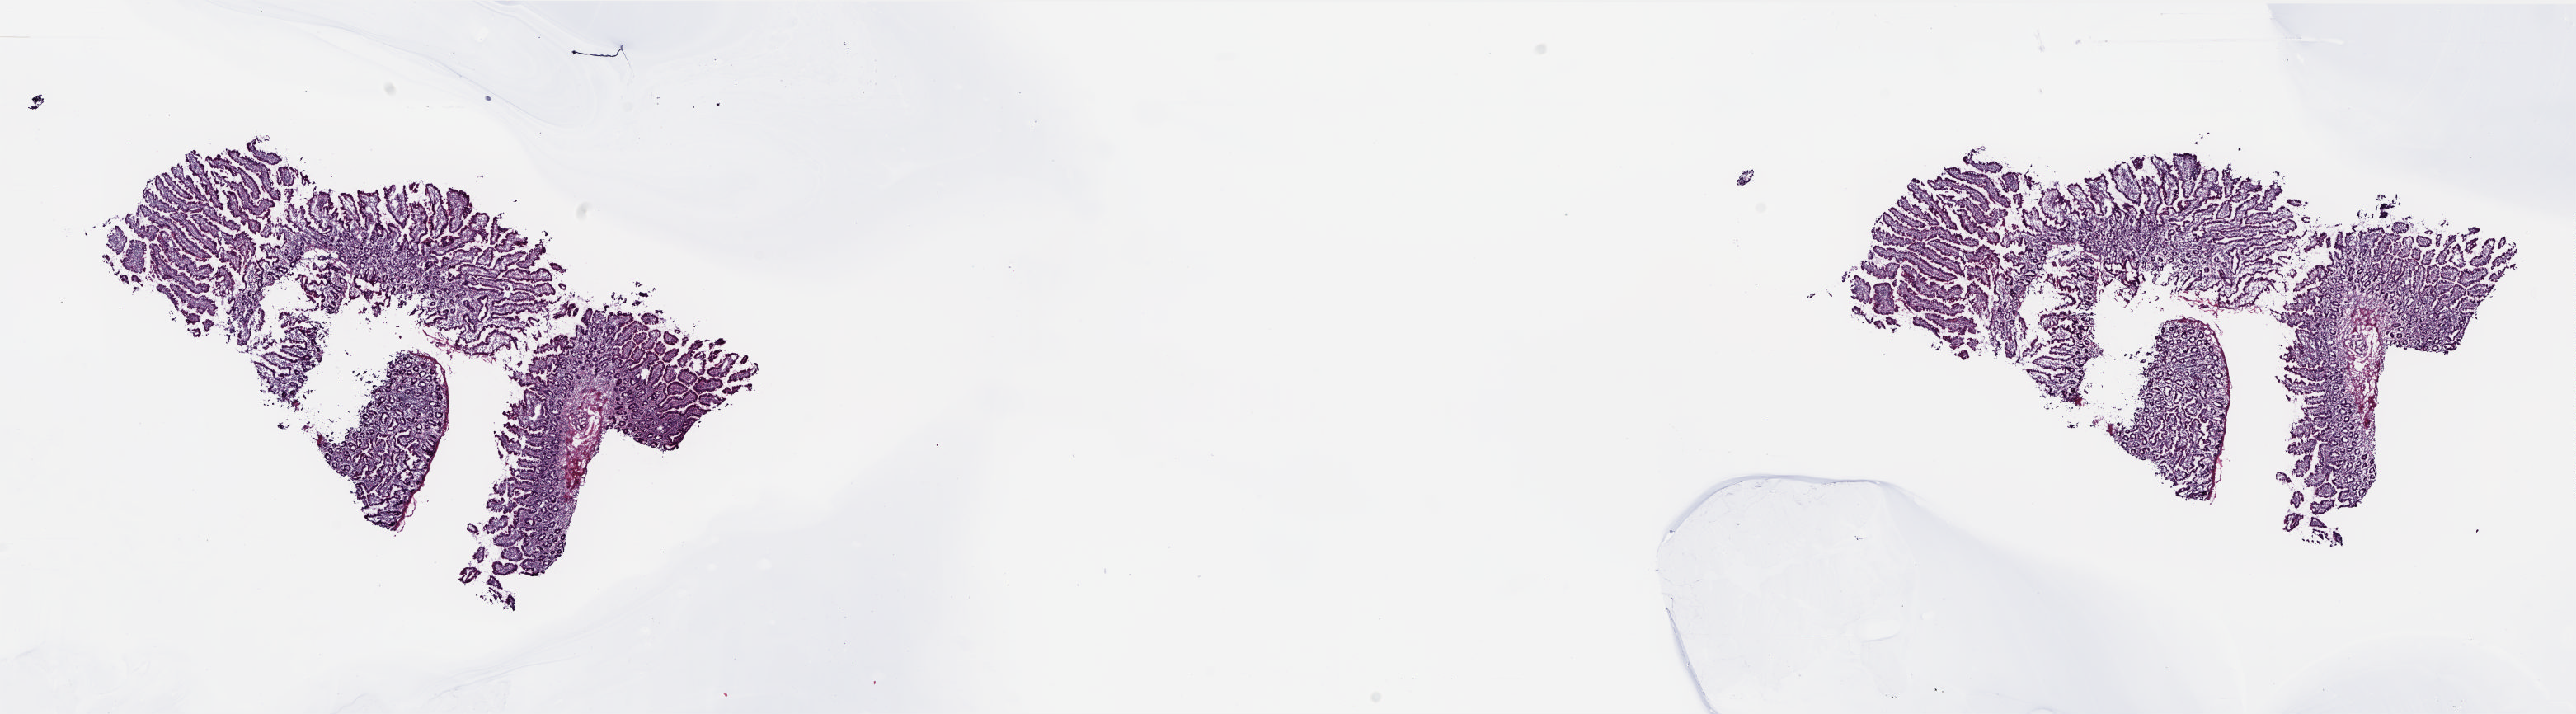
Whole-slide histology image, H&E-stained — shown as a low-resolution overview of the whole scanned area (about 25.0 x 6.9 mm, acquisition: 20x scan). Frozen section from the top of the tissue portion. Solid tissue normal (non-tumour tissue) sample from the pancreas. Male patient; age at initial diagnosis 76 years. Pathologist review of this section (percent, as recorded): tumour cells 0%, tumour nuclei 0%, normal cells 100%, stromal cells 0%, necrosis 0%. Inflammatory infiltration, as recorded: lymphocyte infiltration 5%, monocyte infiltration 0%, neutrophil infiltration 0%.
- this section: solid tissue normal sample (biorepository sample class)
- patient diagnosis: Infiltrating duct carcinoma, NOS